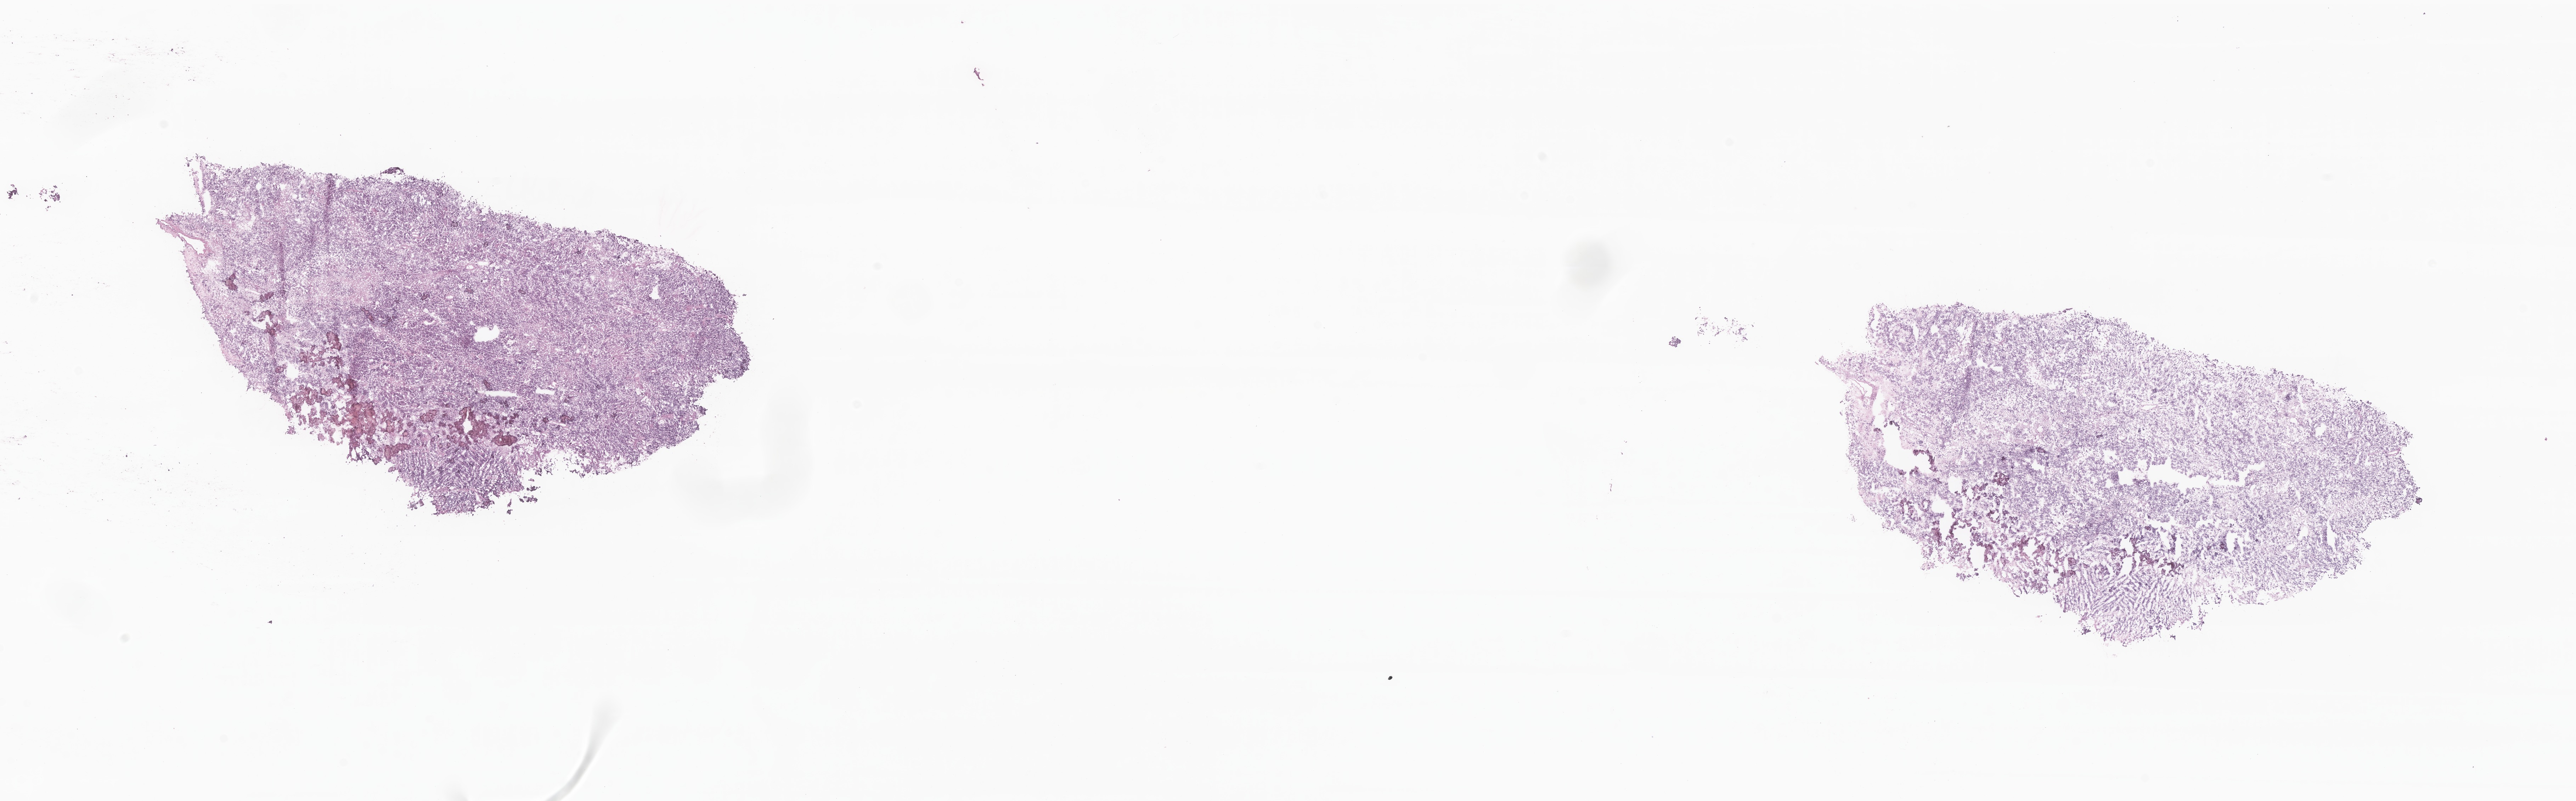
Digitized hematoxylin and eosin (H&E)-stained section of tumor tissue from the brain, shown as a low-resolution overview of the whole scanned area (about 30.7 x 9.5 mm). Frozen section. Male patient, age 156 months (13 years).
- diagnosis: Neoplasm, malignant